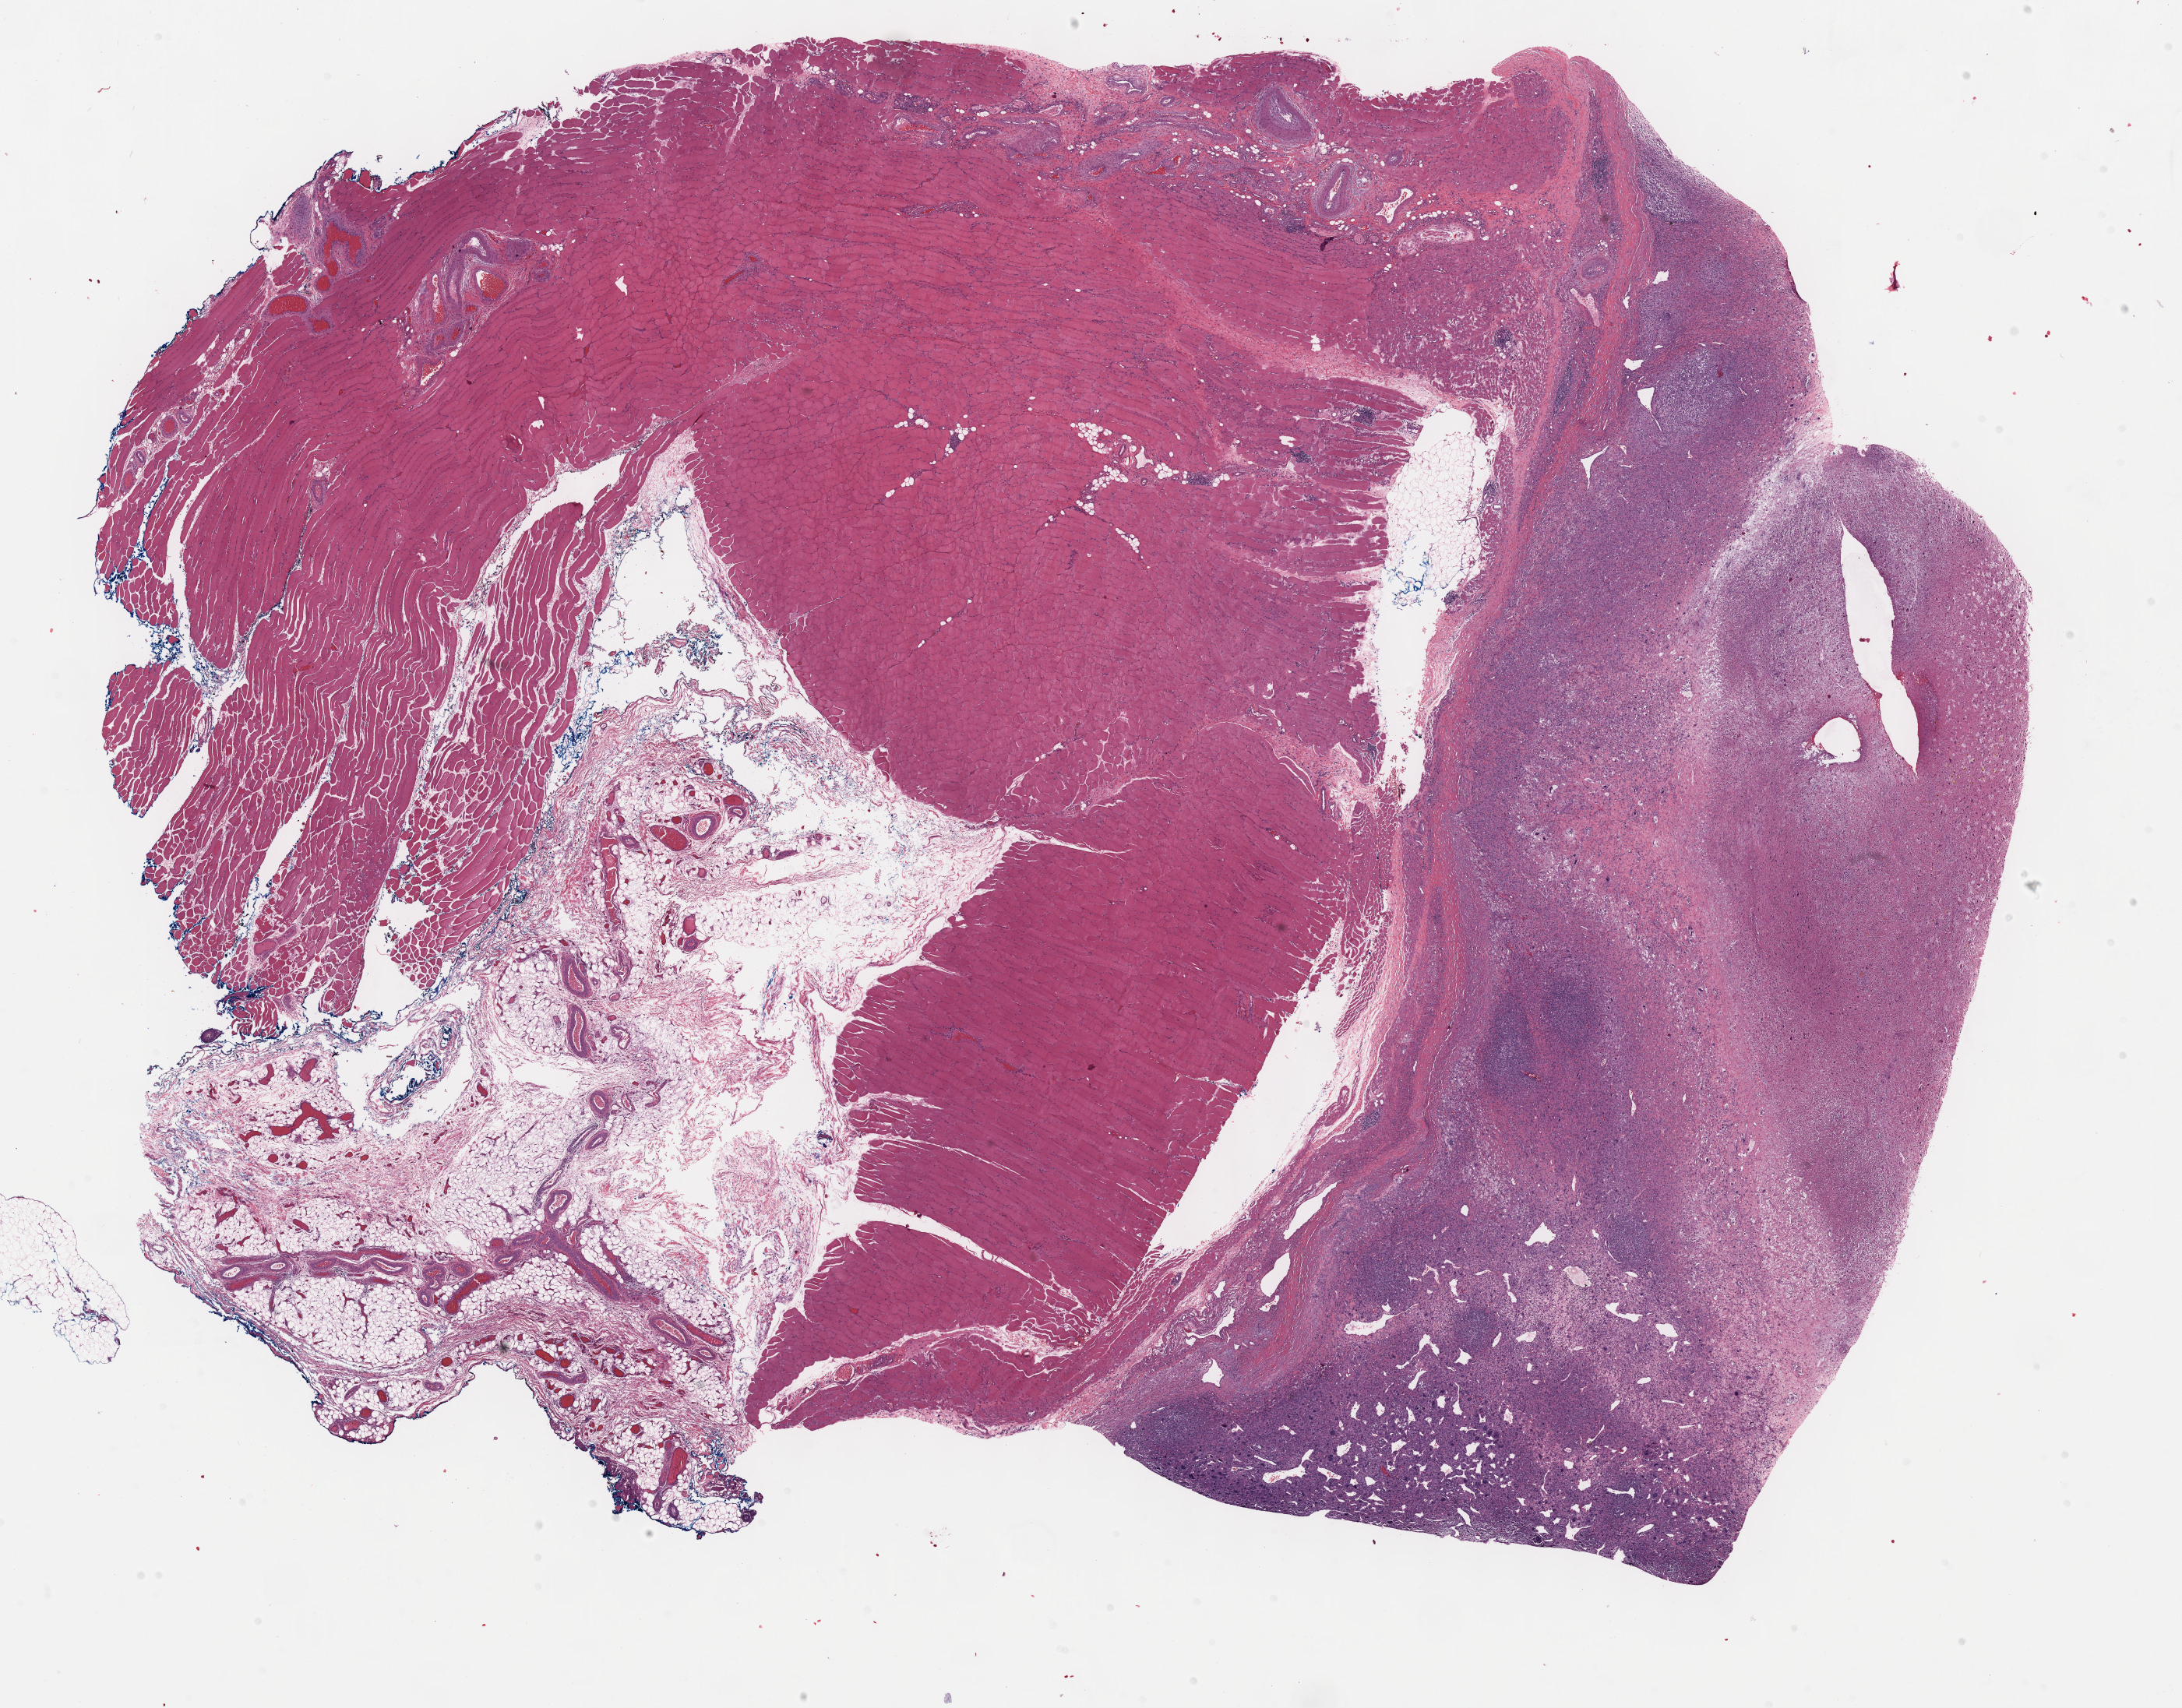
H&E-stained whole-slide image, shown as a low-resolution overview of the whole scanned area (about 22.7 x 17.7 mm). Formalin-fixed paraffin-embedded (FFPE) diagnostic section. Sample: primary tumour, connective, subcutaneous and other soft tissues. Male, age 51 years at initial diagnosis.
Histologic diagnosis: Fibromyxosarcoma (connective, subcutaneous and other soft tissues of thorax).